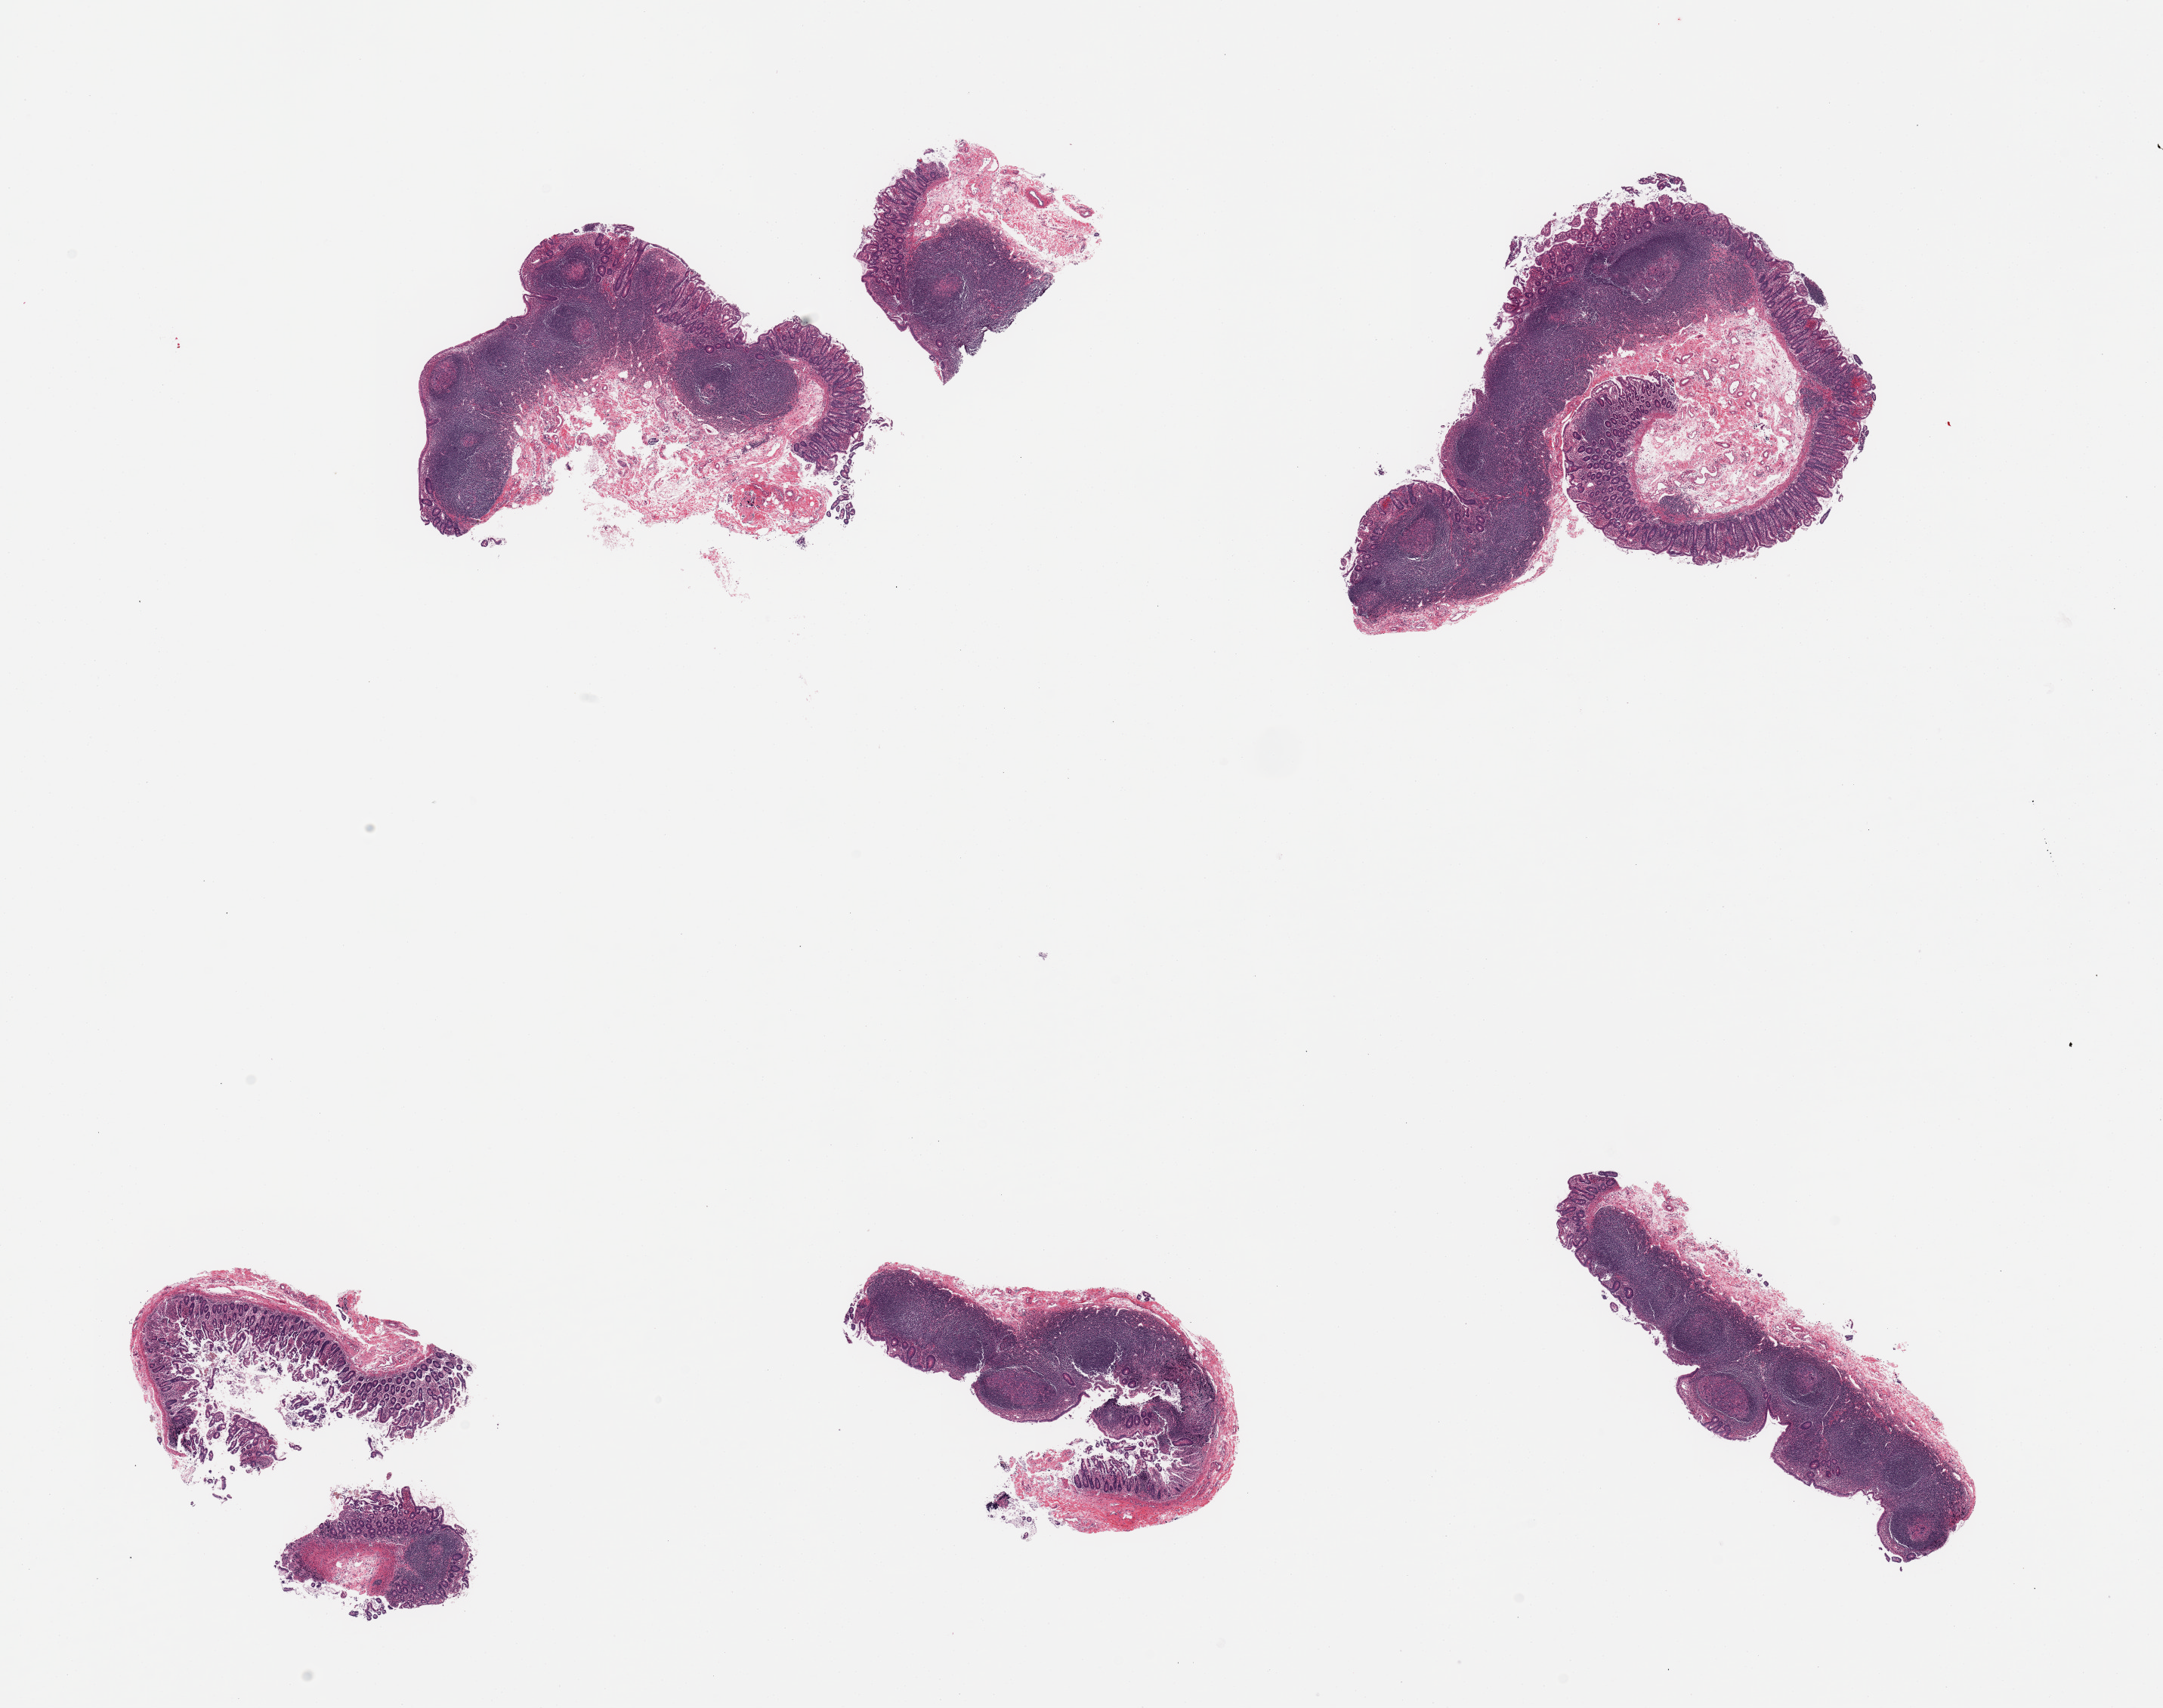
Haematoxylin and eosin whole-slide image, whole scanned area (about 22.6 x 17.9 mm, from a 20x scan) shown as a low-resolution overview. PAXgene-fixed, paraffin-embedded tissue. Sampled site (target tissue): ileum. Donor tissue sample. Donor sex: male.
Pathologist's review note for this sample: 6 pieces; abundant lymphoid tissue.